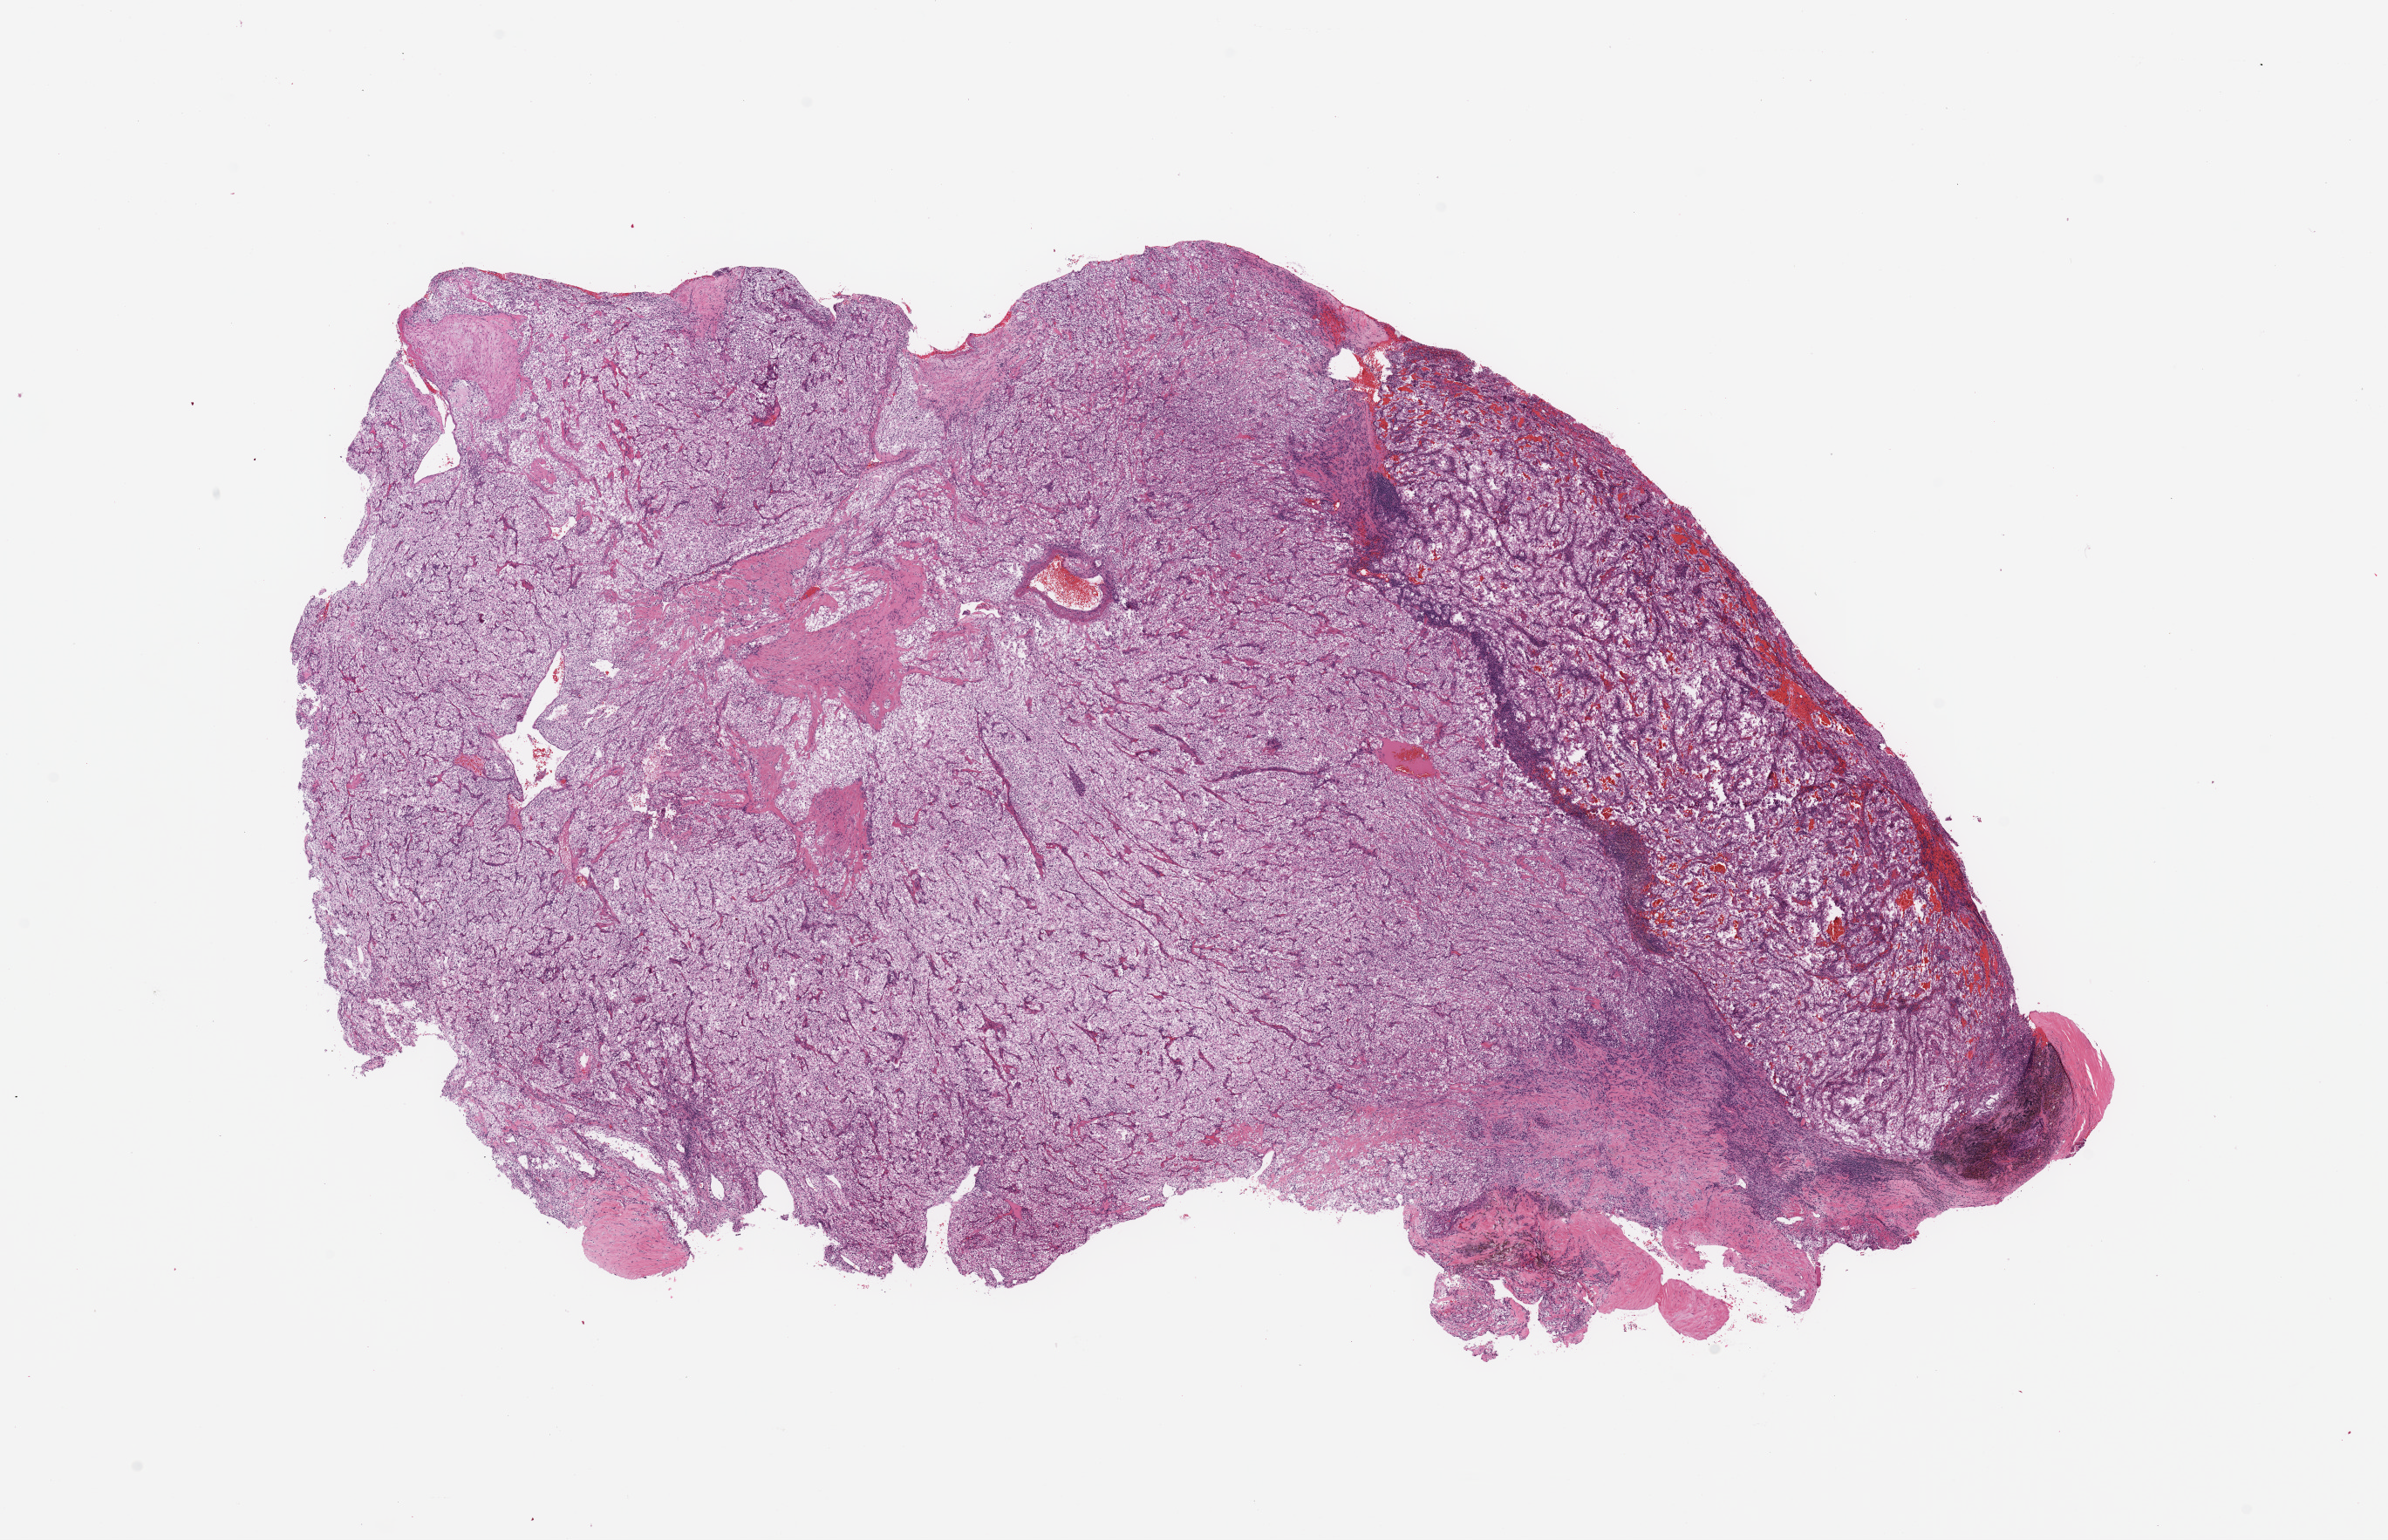
Whole-slide histology image, H&E, whole scanned area (about 21.7 x 14.0 mm) shown as a low-resolution overview. Kidney, tumour tissue. Male, 40 y/o. Histologic grade: G3 (poorly differentiated).
Histologic diagnosis: Renal cell carcinoma, NOS. AJCC pathologic stage: IV.